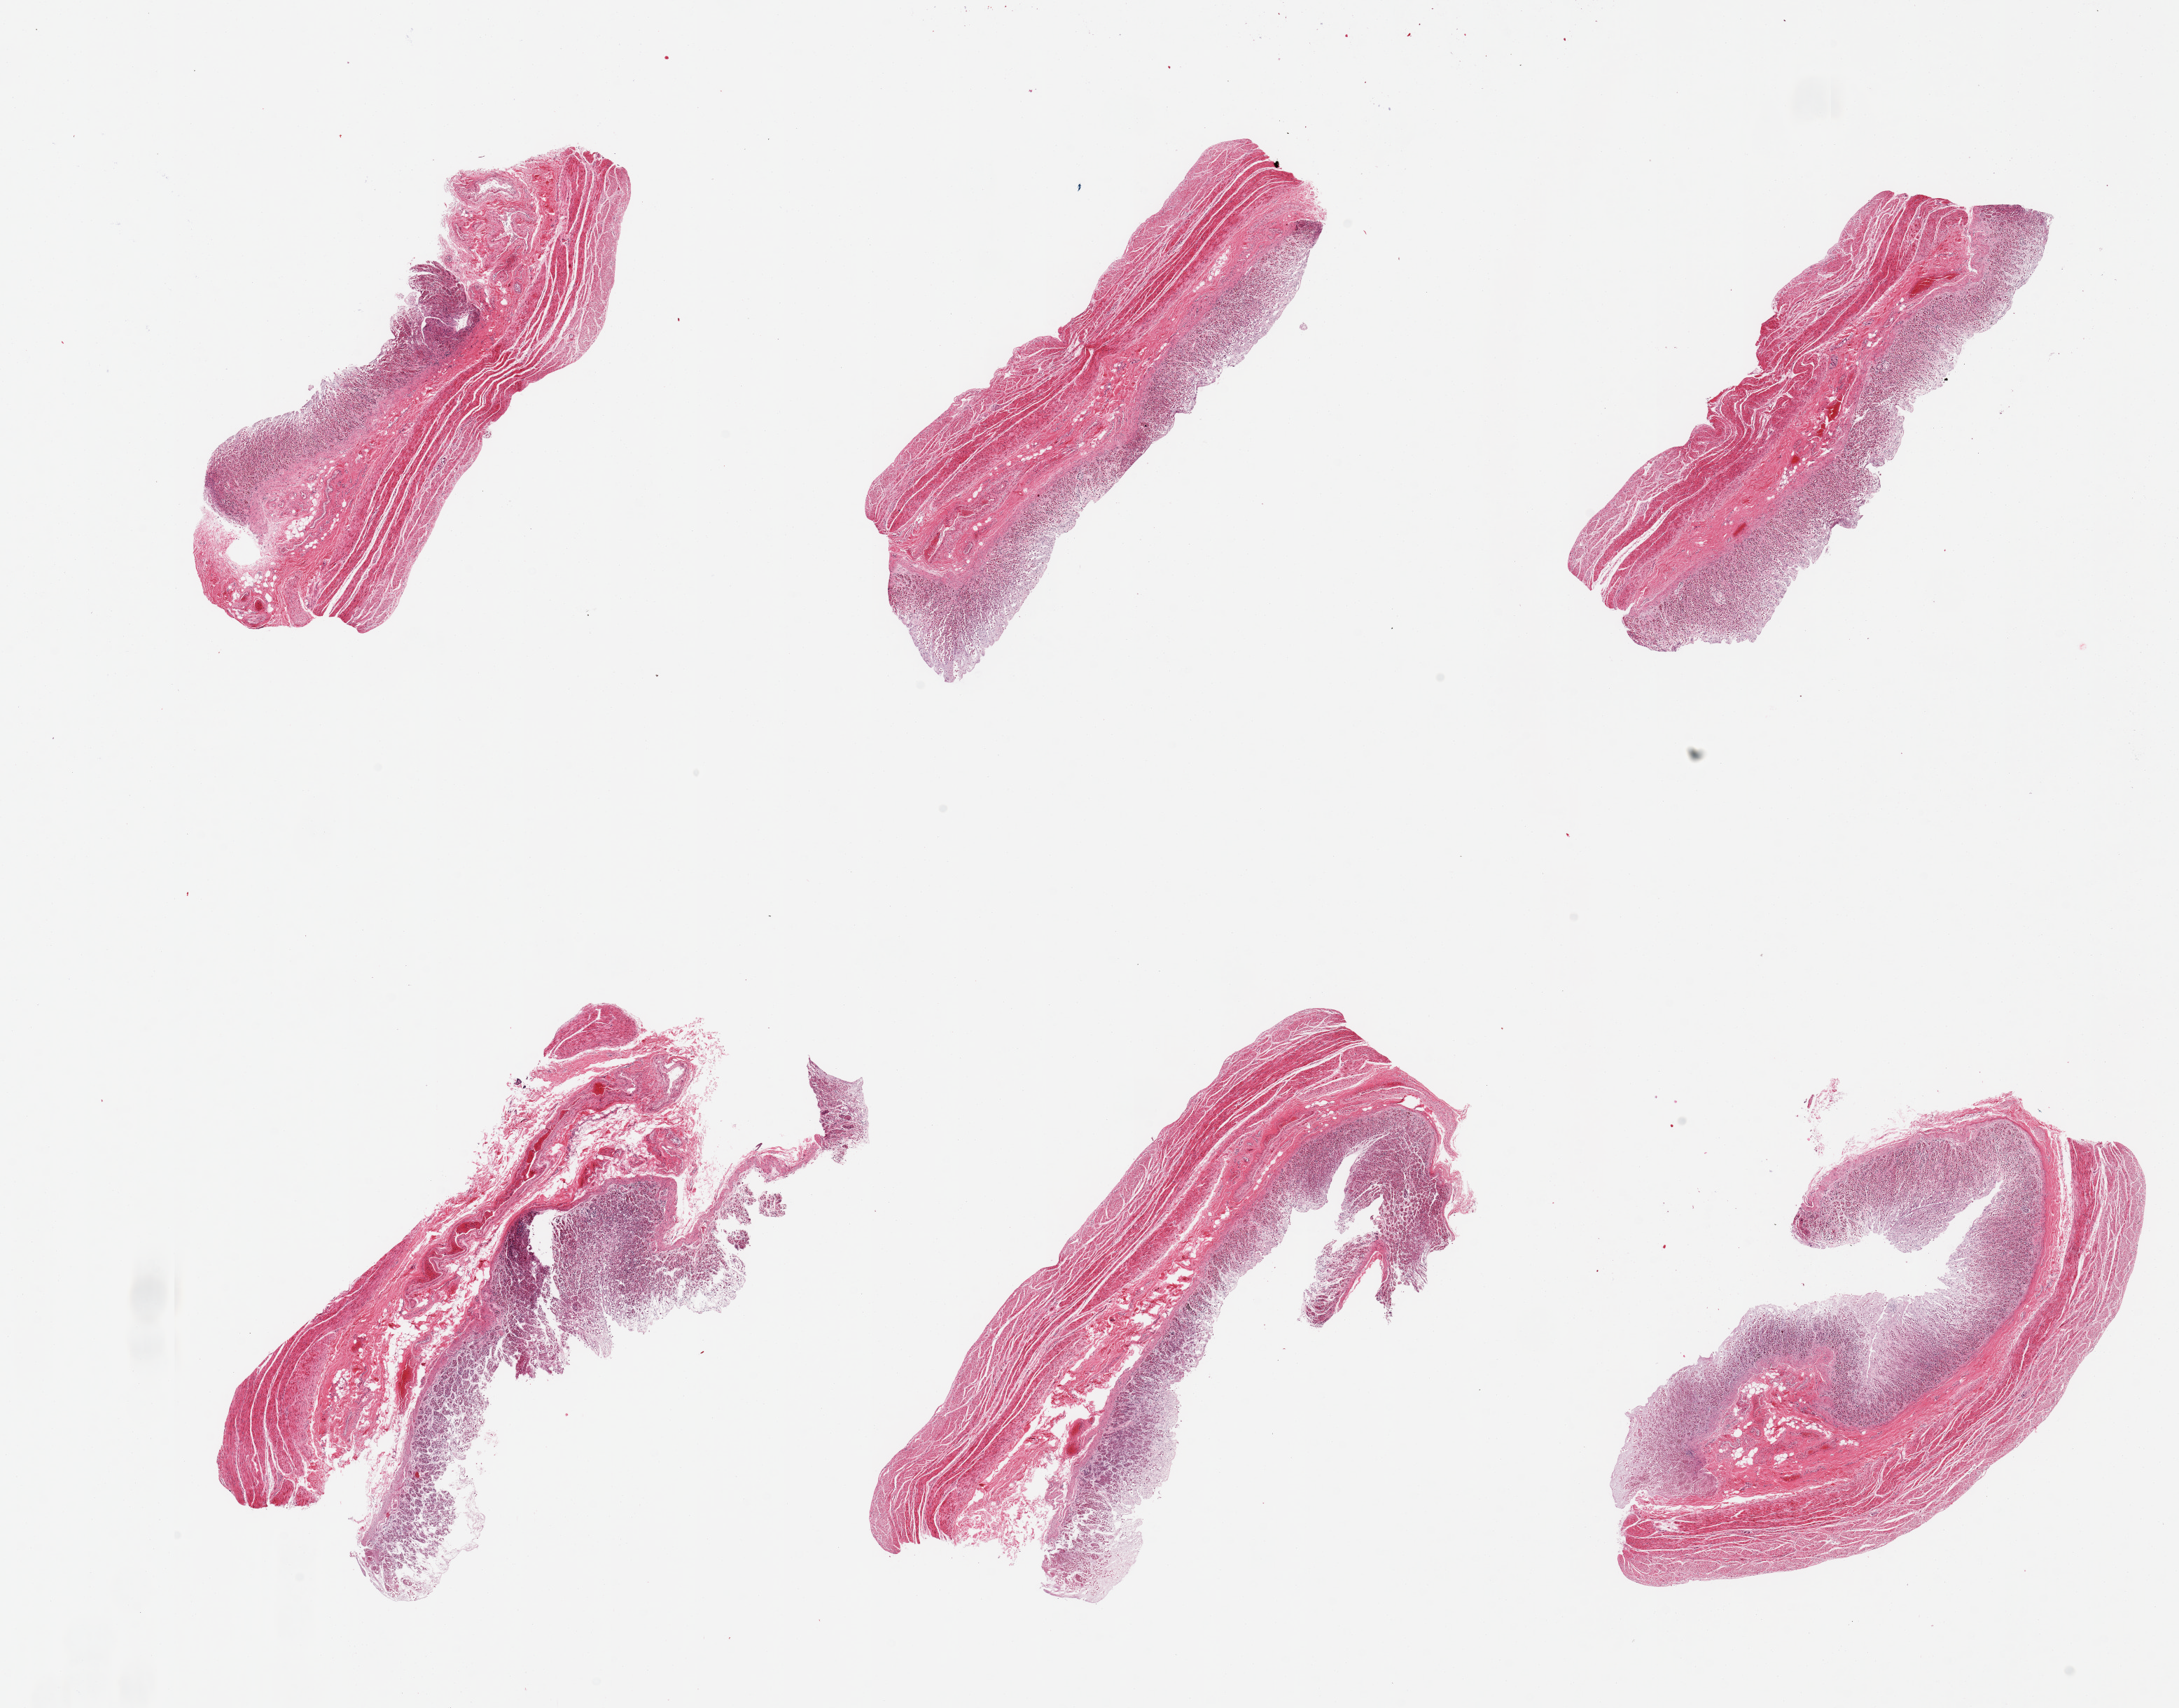
Whole-slide image, haematoxylin and eosin stain — whole scanned area (about 24.6 x 19.3 mm, from a 20x scan) shown as a low-resolution overview. PAXgene-fixed paraffin-embedded (PFPE) section. Target tissue: stomach. Tissue donor sample. Donor: female.
• review note (as recorded): 6 pieces; mucosa severely autolyzed; muscularis moderately autolyzed